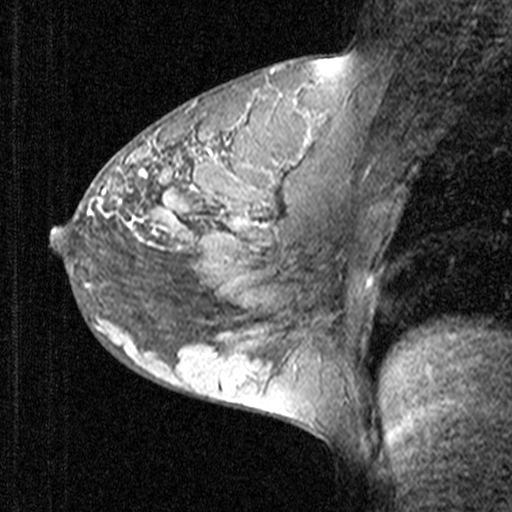
Breast MRI (dynamic contrast-enhanced), one sagittal slice. Slice 26 of 44 in the series (ordered by position). Dynamic contrast-enhanced study with each time point stored as its own series, time point 2 of 3 at this slice position (early post-contrast, ordered by acquisition time). 1.5 T. TE 4.5 ms, TR 11 ms. 3 mm slice thickness. 512 × 512 image matrix, field of view 200 × 200 mm. Patient: female, 27 years. From the clinical record (not read from this slice): setting: breast cancer imaged before/during neoadjuvant chemotherapy; receptor status: HR-positive, HER2-negative.
Annotated regions visible in this slice (semi-automatic segmentation, software-assisted and operator-edited):
- analysis volume of interest (the breast-tissue region the enhancement analysis was run in; not a lesion): box from (x=68, y=146) to (x=165, y=239) px
- tumour enhancement mask (voxels above the 90 % enhancement threshold inside the analysis volume of interest): (x=103, y=170)–(x=157, y=196)